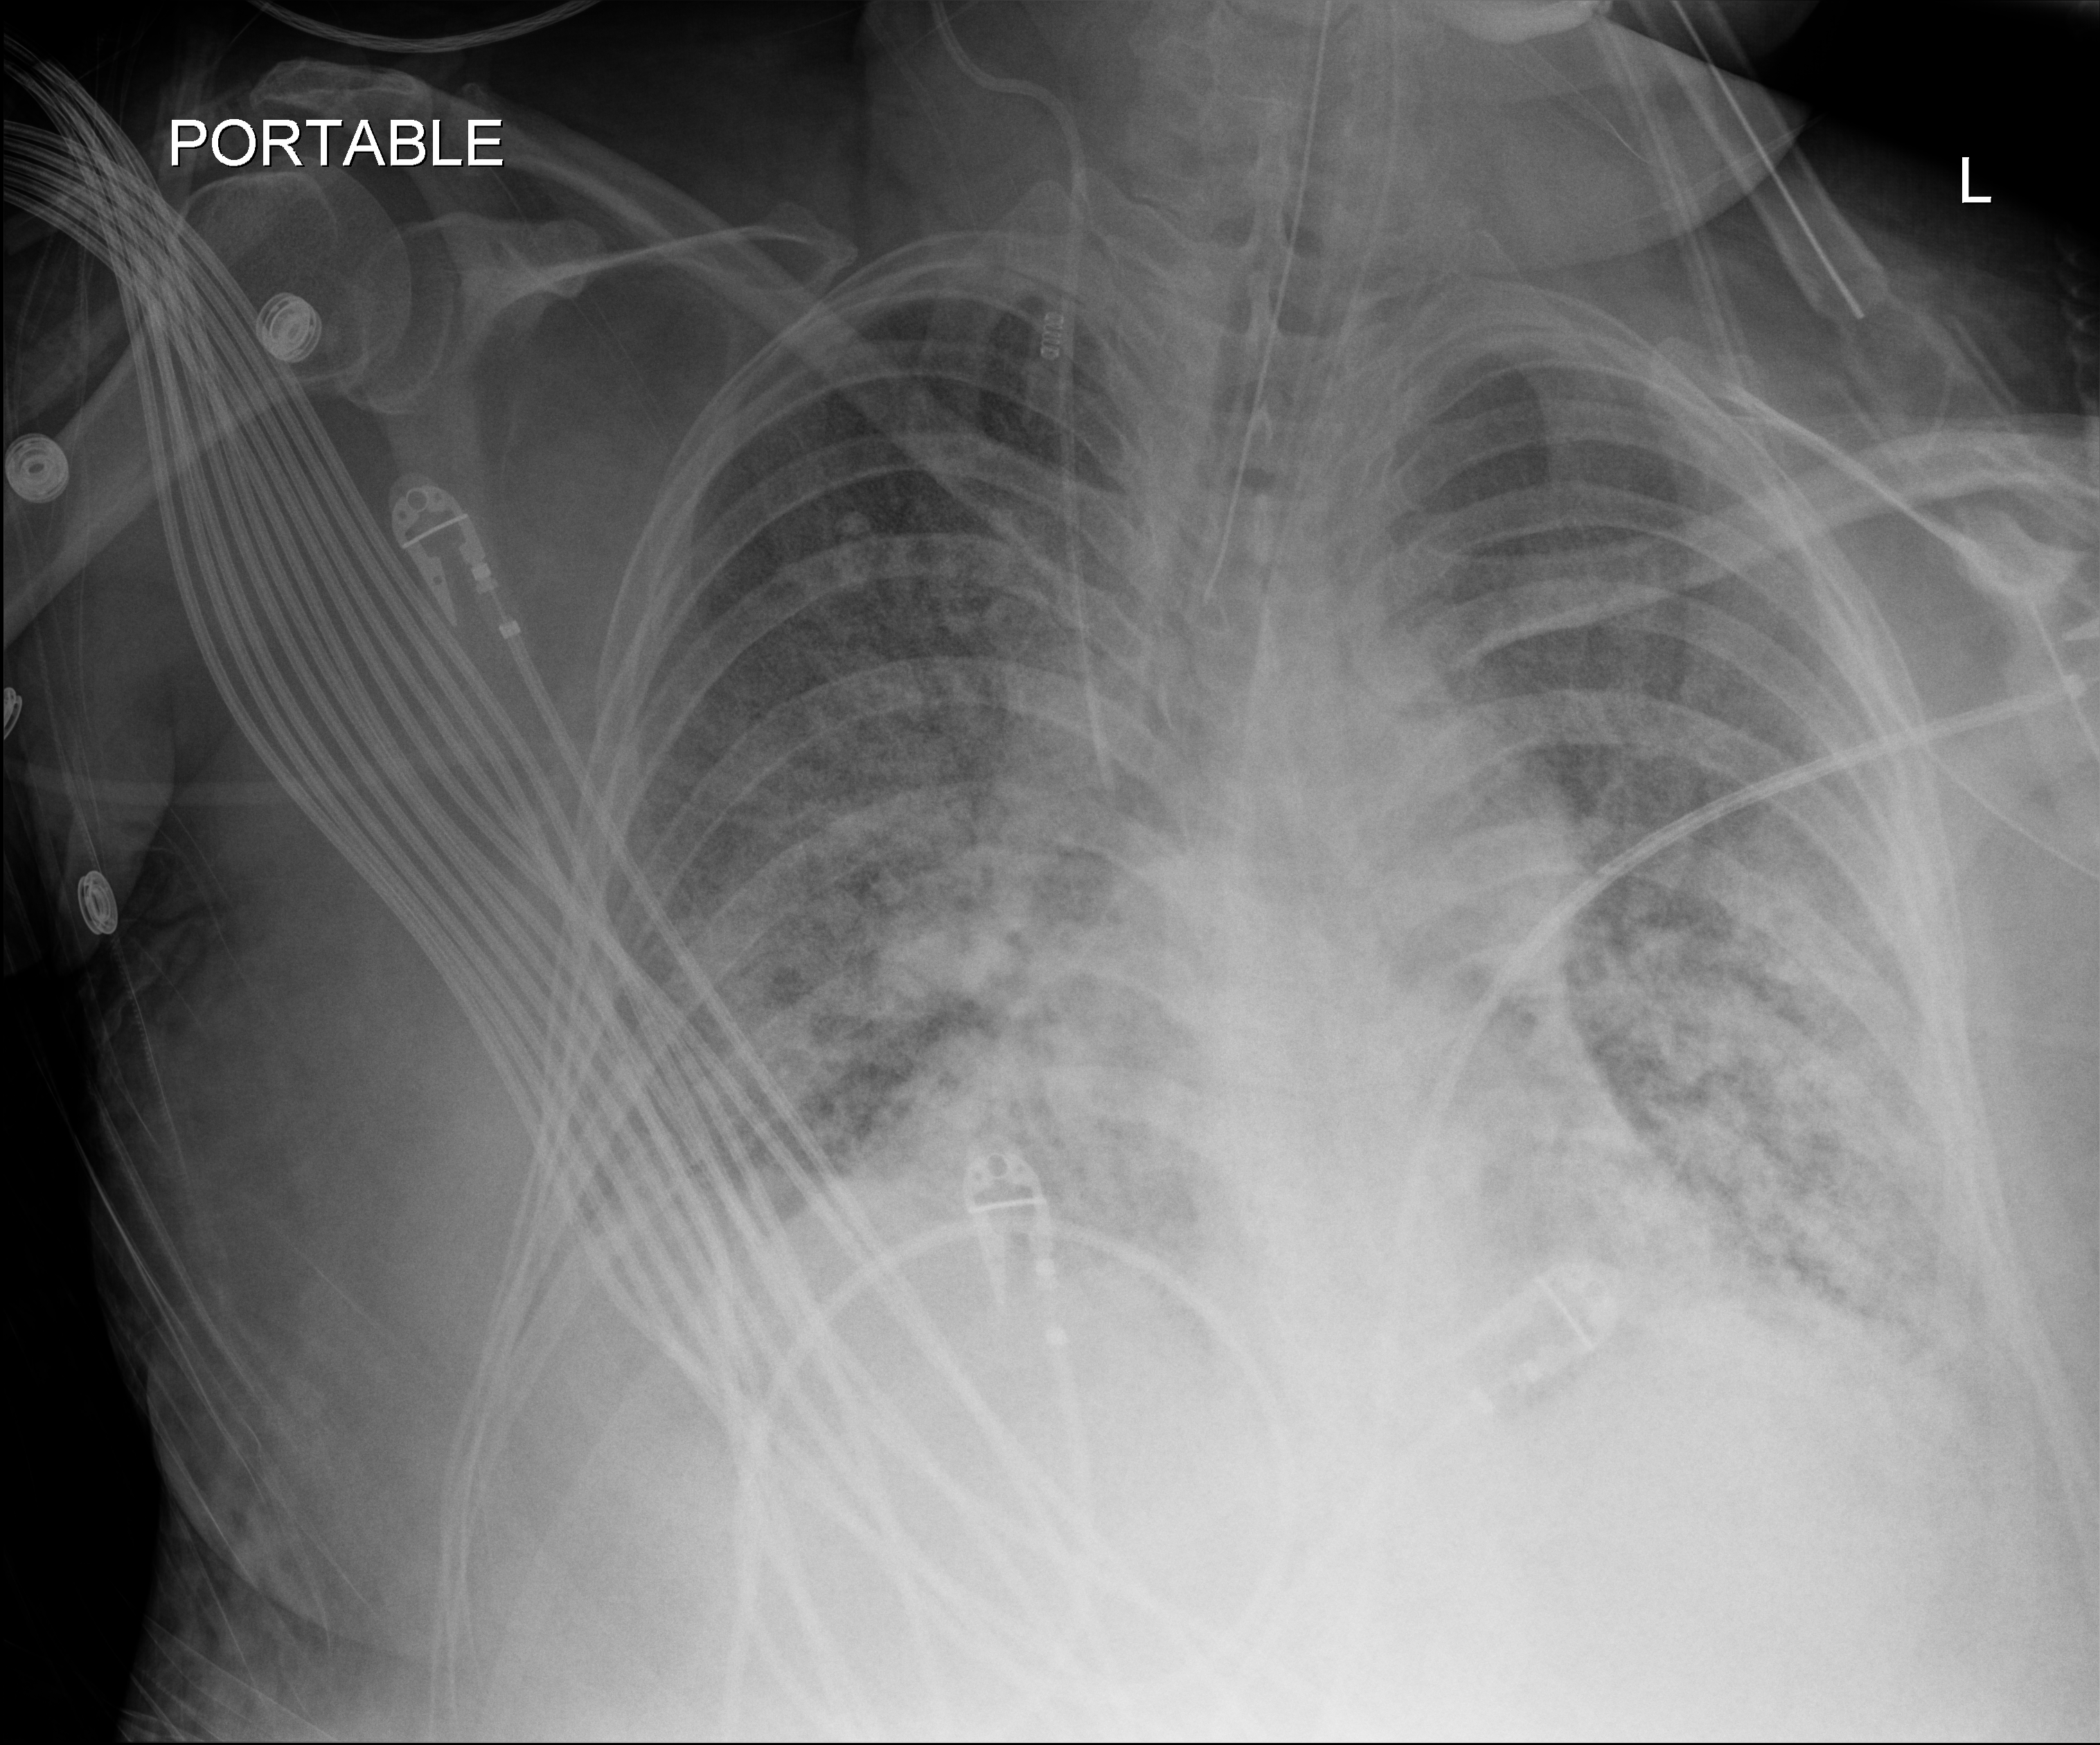
Portable chest radiograph, anteroposterior (AP) projection. Adult patient hospitalised with COVID-19, age 18–59 years.
From the hospital-stay record, not from the radiograph (when in the stay this image was taken is not recorded):
- mechanically ventilated during this hospital stay: yes